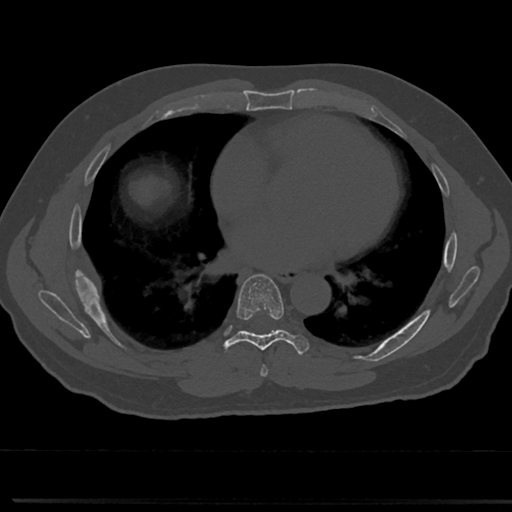
CT including the spine, one axial slice. Position 405 of 817 along the scan axis. 120 kVp. Bone window (W 1800 / L 400 HU). 0.5 mm slice thickness. 512 × 512 image matrix, field of view 355 × 355 mm. Male patient, age 61 years. Case-level facts recorded for this patient, not image findings: primary cancer: prostate.
Annotated regions visible in this slice (semi-automatic segmentation, software-assisted and operator-edited):
- T6 vertebra: bounding box [x1, y1, x2, y2] px = [260, 340, 319, 371]
- T7 vertebra: [215, 275, 308, 358]